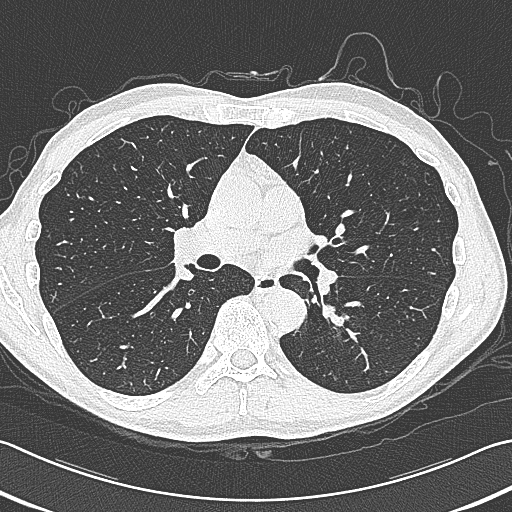
Chest CT (low-dose screening protocol), one axial image; first (baseline) screen; lung window (W 1500 / L -600 HU); lung (sharp) reconstruction kernel (B80f); slice 160 of 354 in the series. Male, age 59 years at enrolment. Former smoker at enrolment.
Expert reader's lesion annotation, bounding box (x1, y1, x2, y2) in pixels: (314, 292, 374, 353). Screening reader's record for this exam (one nodule recorded; not confirmed to be the boxed lesion): non-calcified nodule or mass ≥4 mm, left lower lobe, 15 × 15 mm, smooth margins, soft tissue attenuation. Official screen result: positive, change unspecified: nodule(s) >= 4 mm or enlarging nodule(s), mass(es), or other non-specific abnormalities suspicious for lung cancer. Participant outcome: lung cancer diagnosed 17 days after this screen — squamous cell carcinoma, large cell, nonkeratinizing, NOS, left lower lobe, poorly differentiated (G3), stage IB (AJCC 6th edition), 31 mm at pathology.